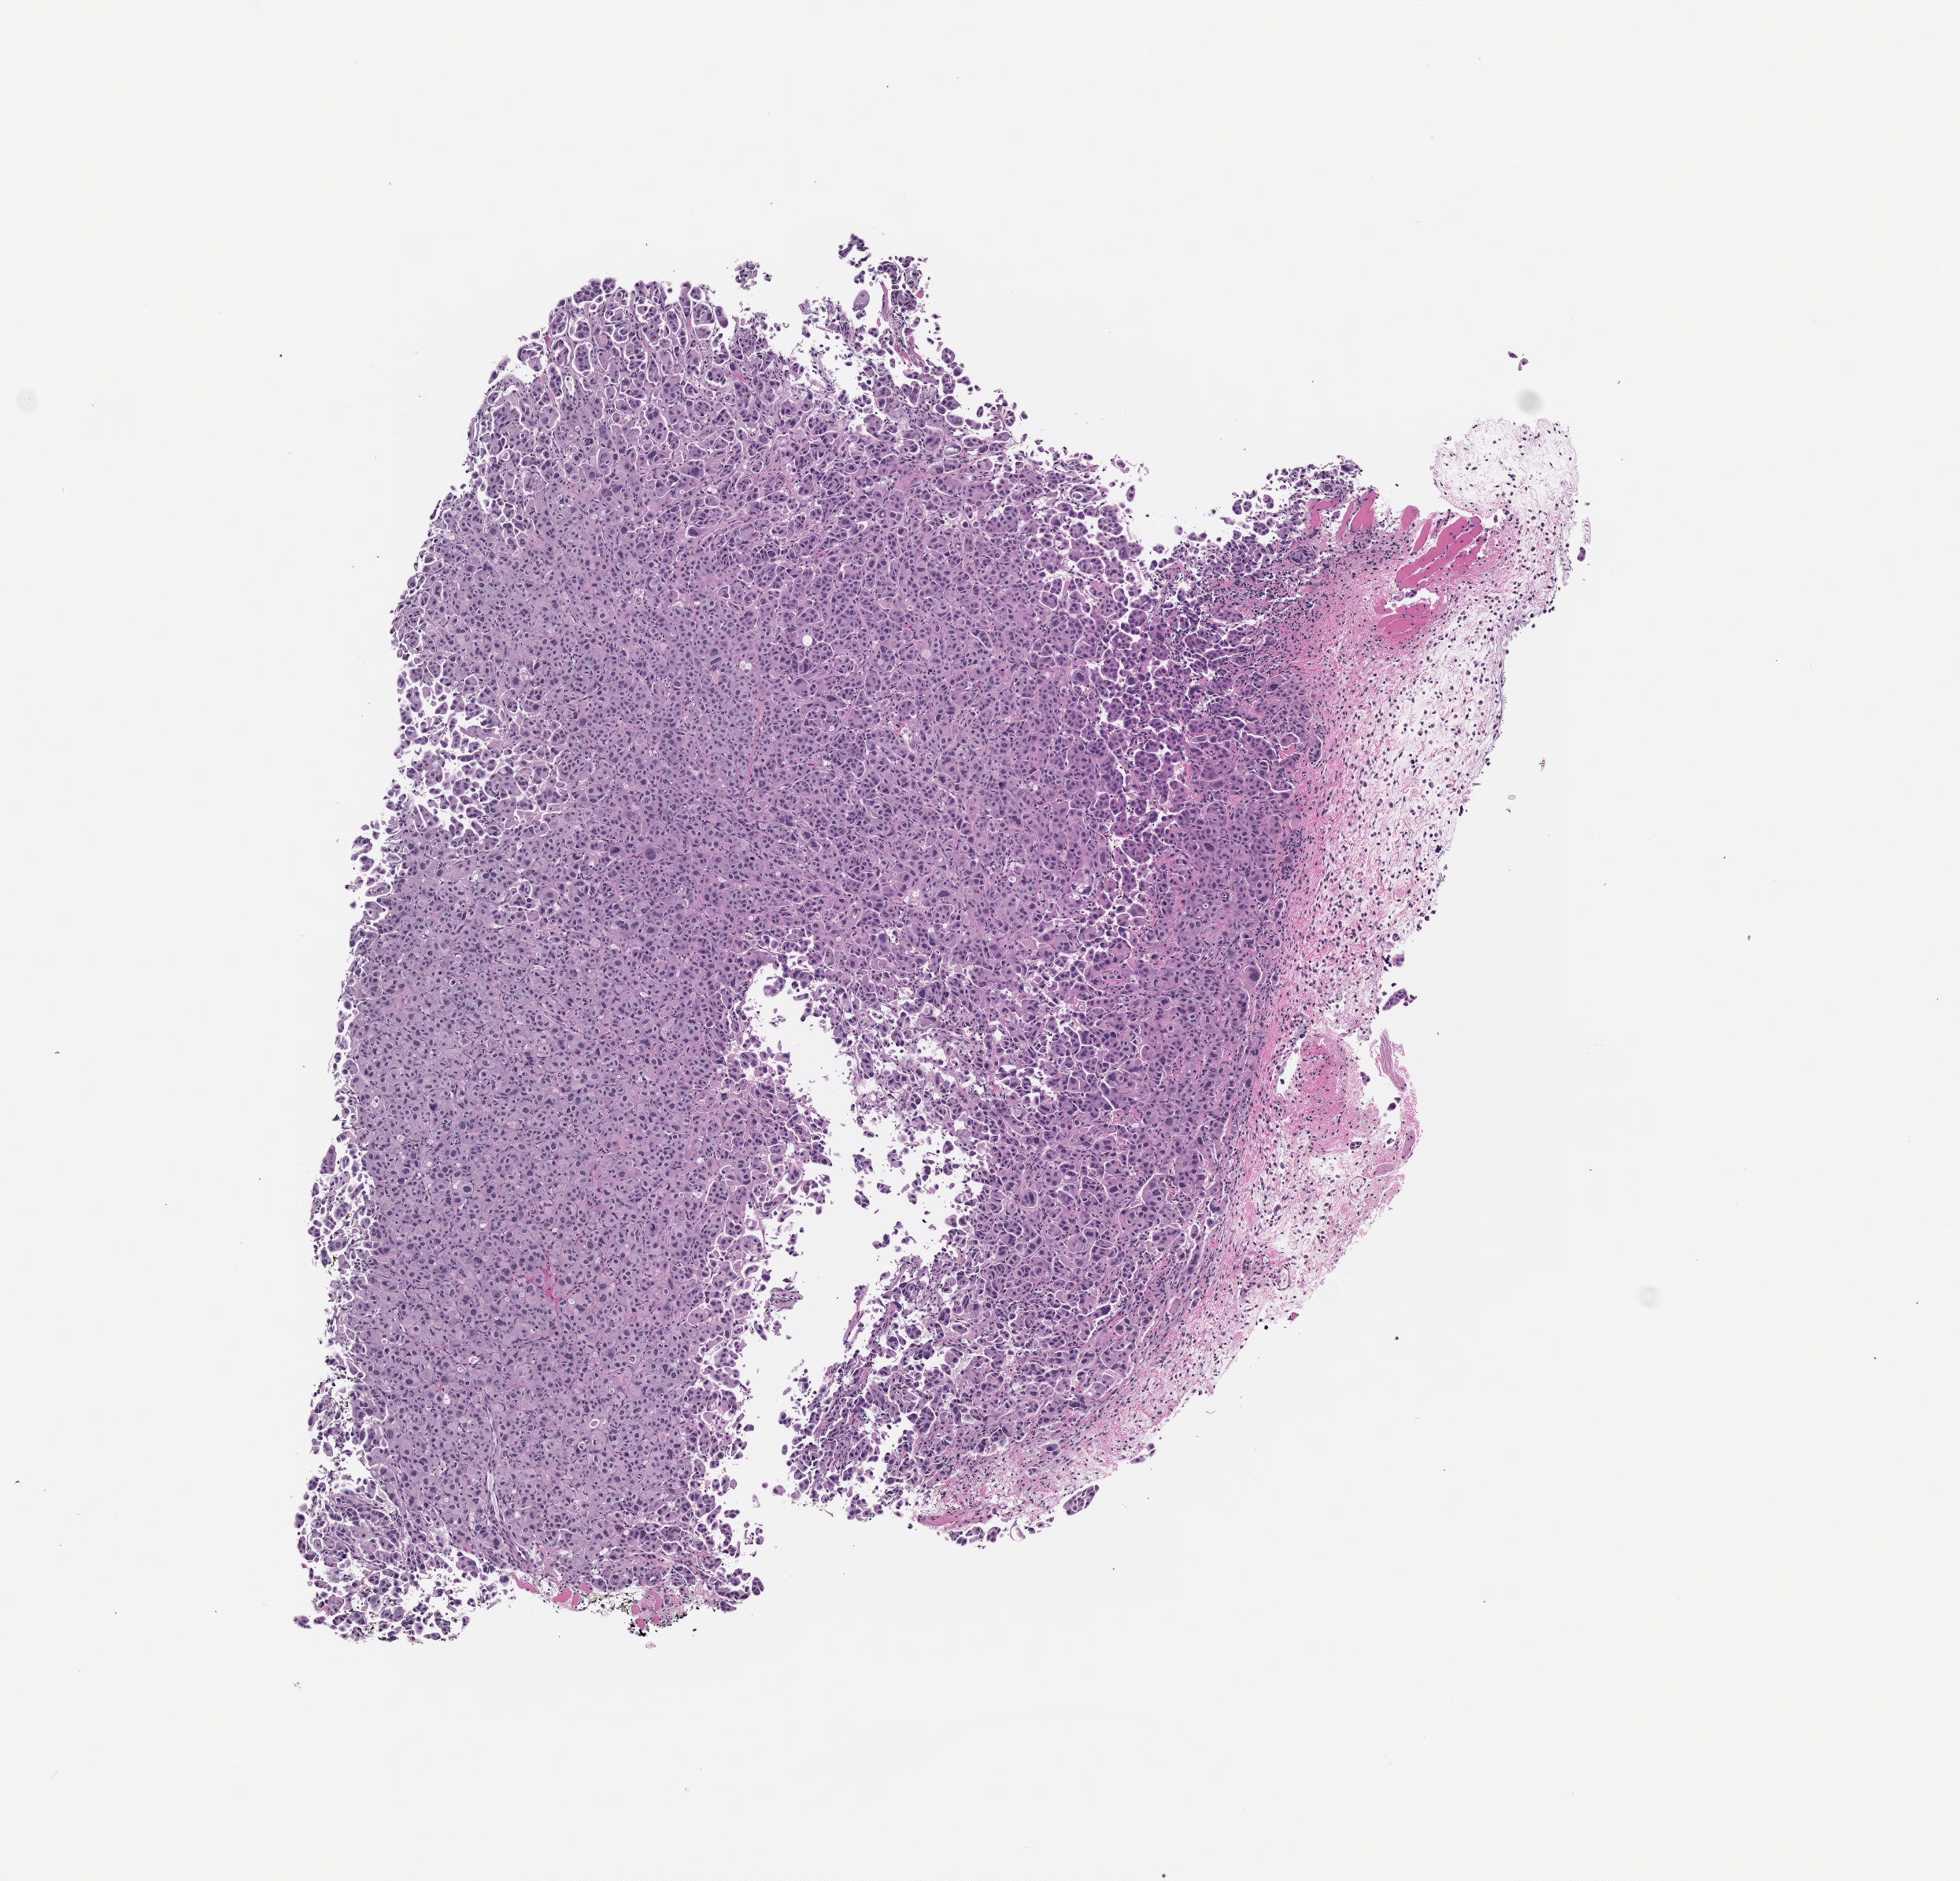
Haematoxylin and eosin whole-slide image of a patient-derived xenograft (PDX) tumor grown in a mouse — whole scanned area (about 5.0 x 4.8 mm) shown as a low-resolution overview; FFPE section; tumor site category: lung.
* originating patient diagnosis: Lung Squamous Cell Carcinoma